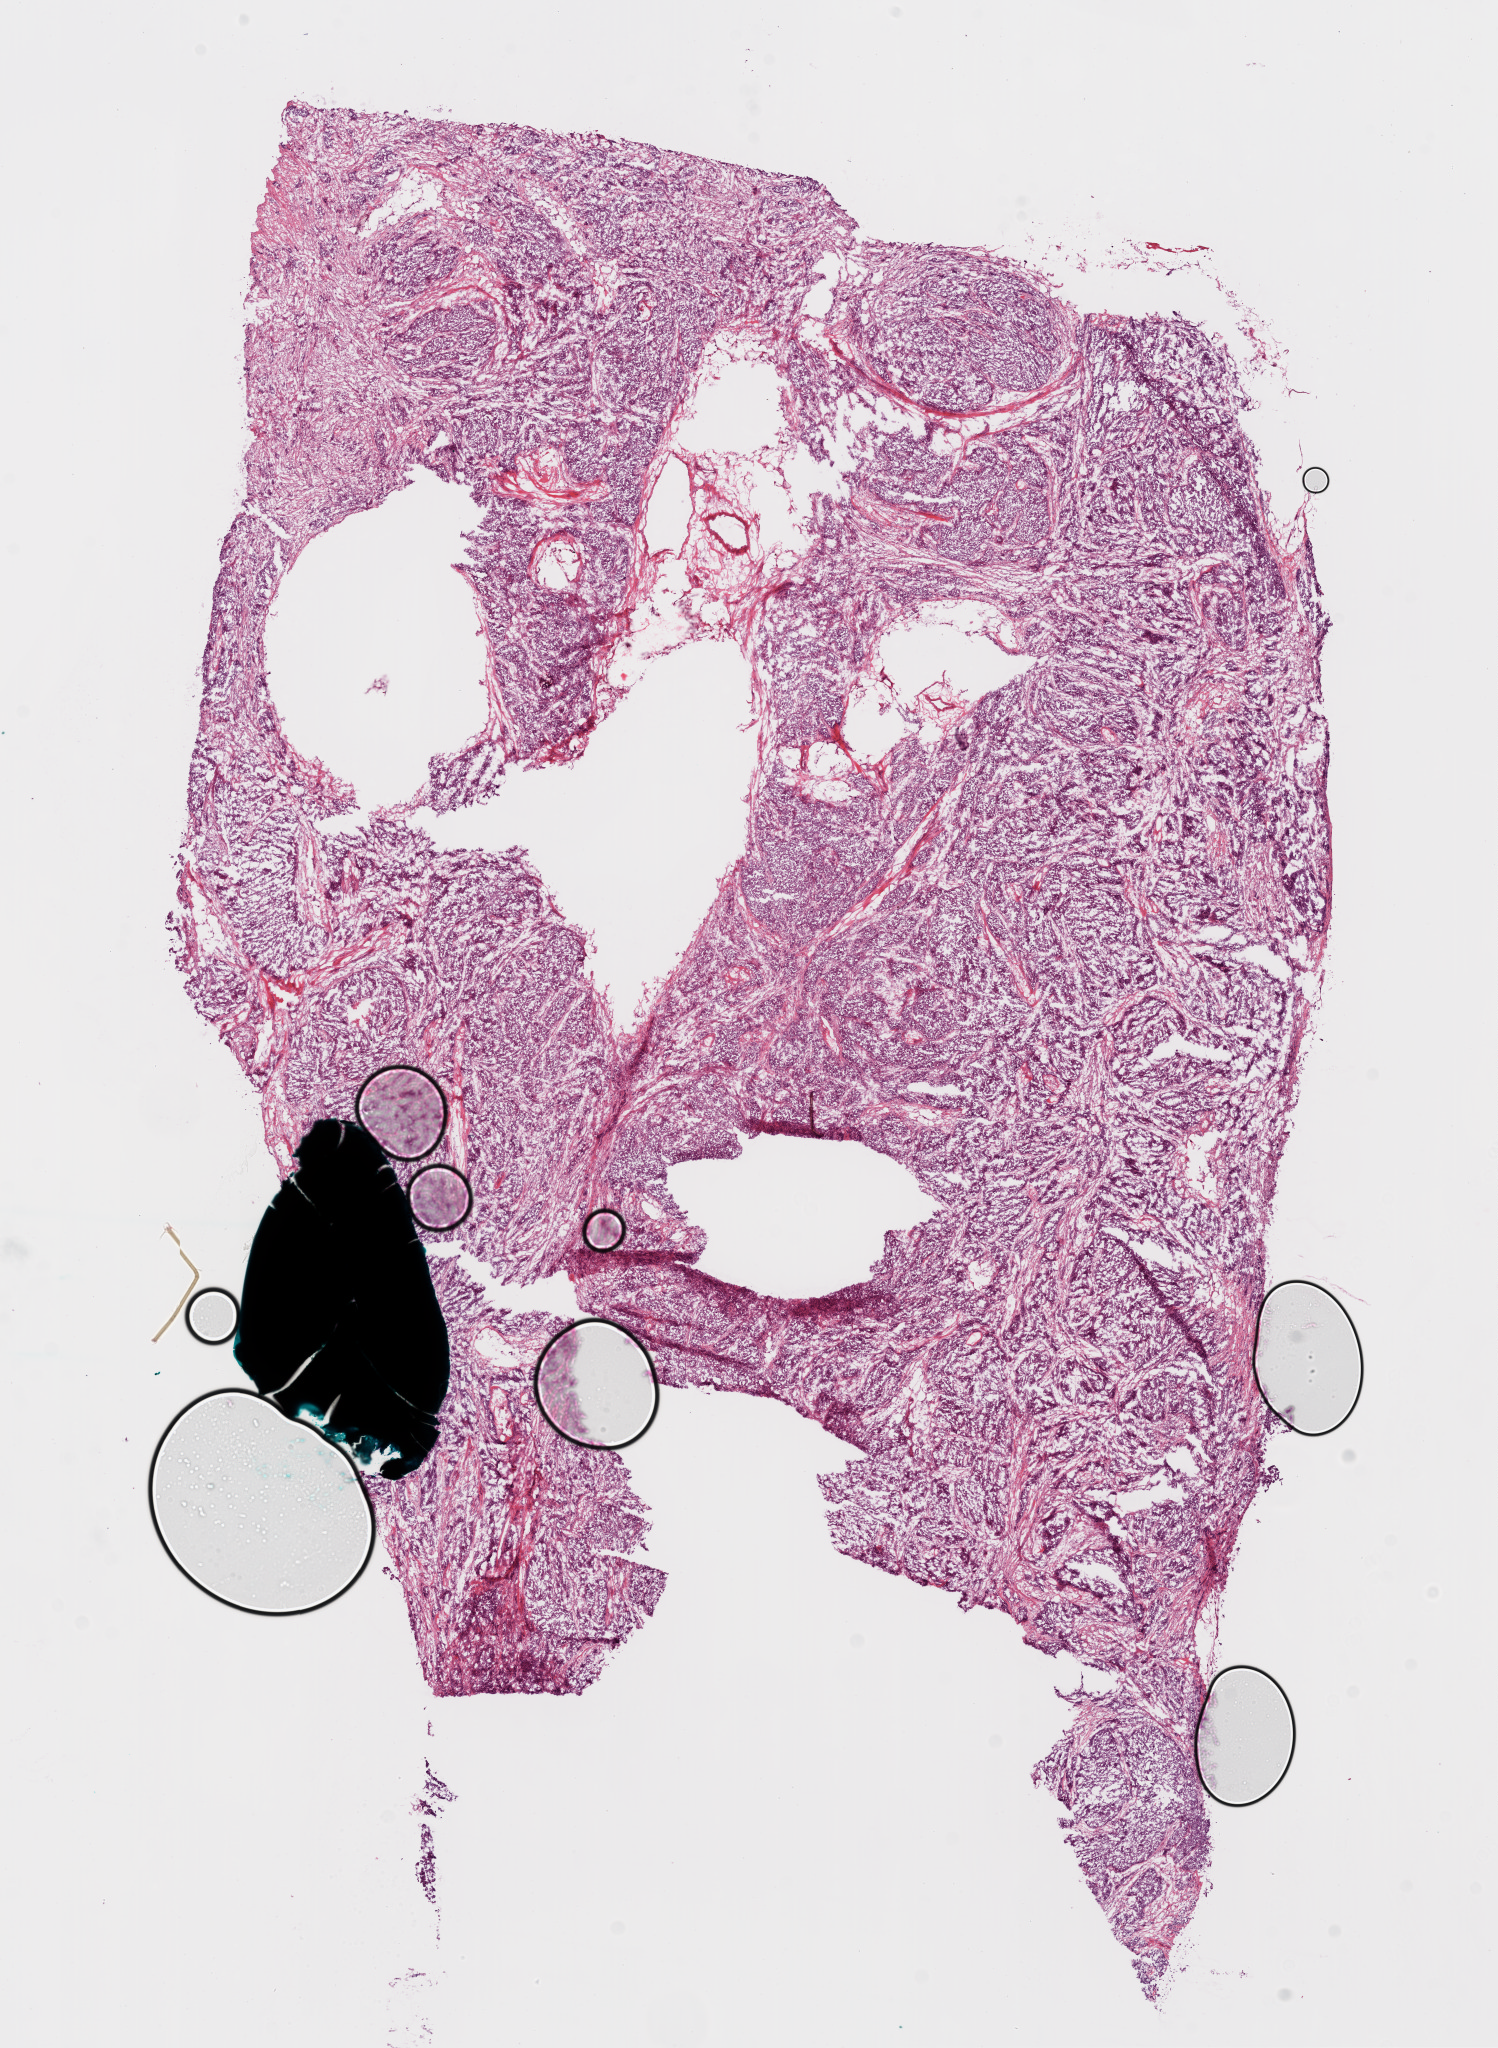
H&E whole-slide image, low-resolution overview of the scanned area, about 12.1 x 16.5 mm (slide scanned at 20x). Slide review estimates, as recorded: tumour cells 90%, tumour nuclei 95%, normal cells 0%, stromal cells 5%, necrosis 5%. Inflammatory infiltration, as recorded: lymphocyte infiltration 100%.
• specimen: frozen section; ovary, primary tumour sample